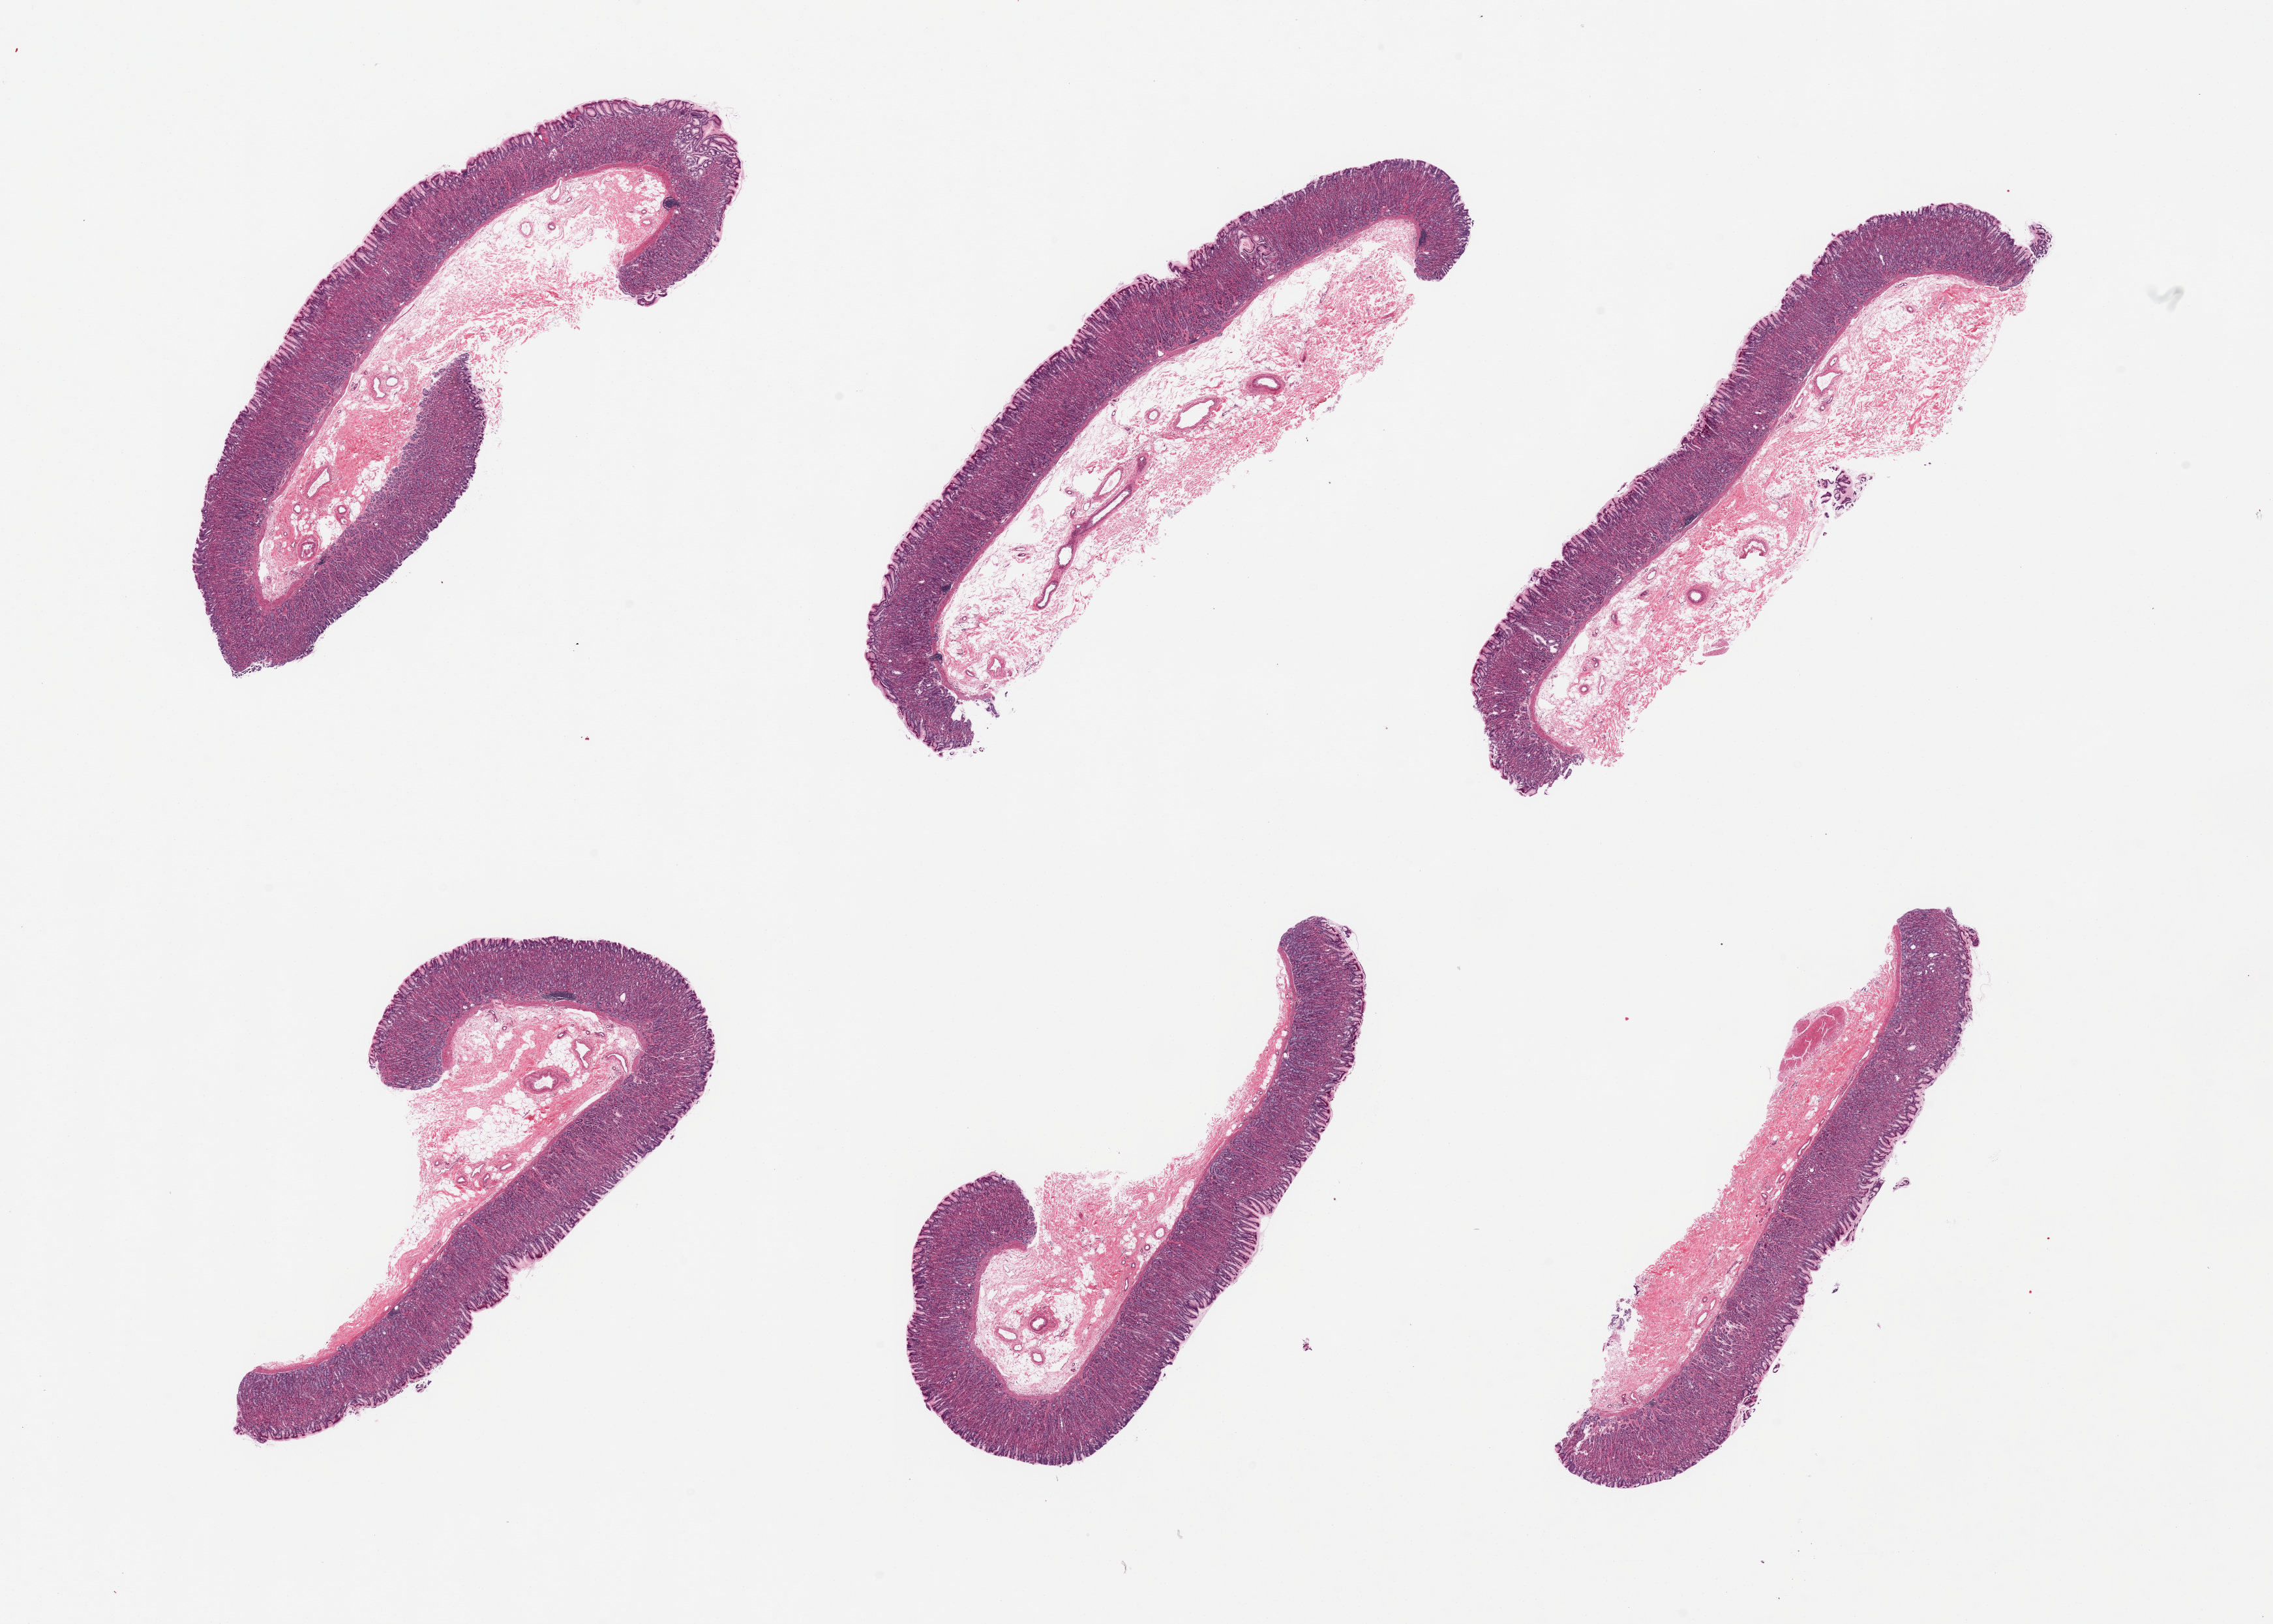
Haematoxylin and eosin whole-slide image — low-resolution overview of the scanned area, about 27.6 x 19.7 mm, PAXgene-fixed paraffin-embedded (PFPE) section, section of stomach (target tissue), tissue donor sample. Female donor.
- pathologist's review note for this sample: 6 pieces, mucosa extremely well preserved, up to ~1mm or ~40% thickness